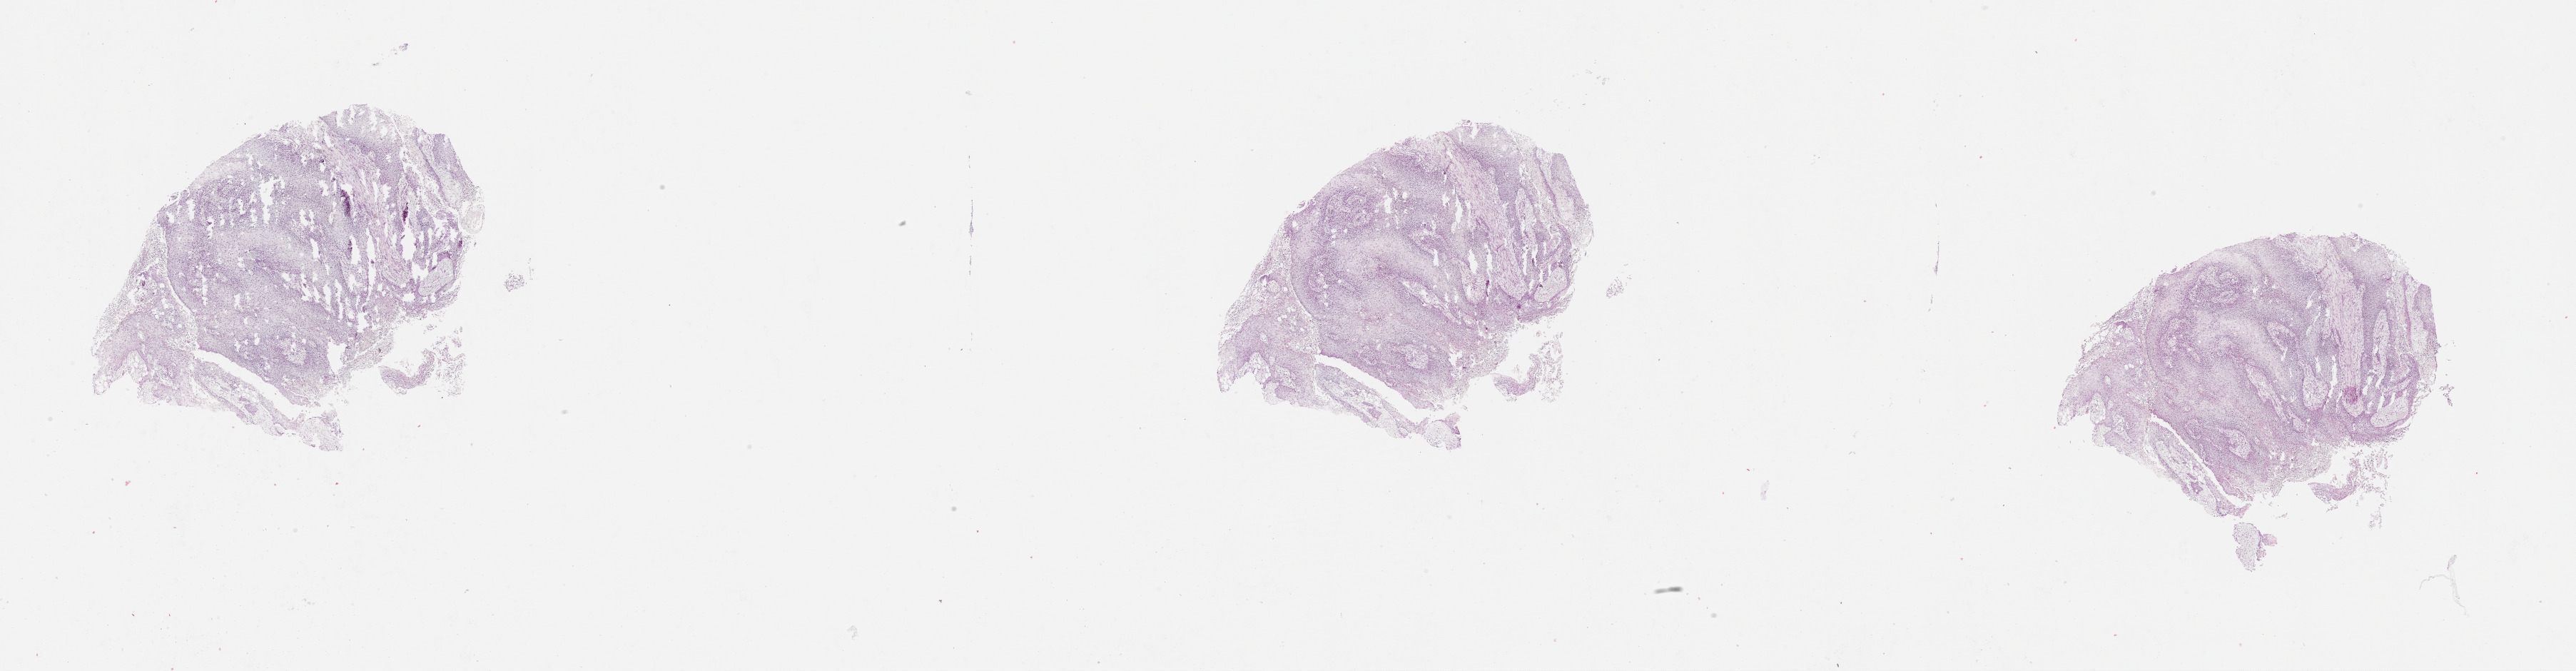
Whole-slide histology image, H&E, low-resolution overview of the scanned area, about 29.1 x 7.6 mm (from a 20x scan), tumour tissue sample, lung. Patient: male, age 69 years.
Patient diagnosis (cohort enrolment): squamous cell carcinoma (lung).